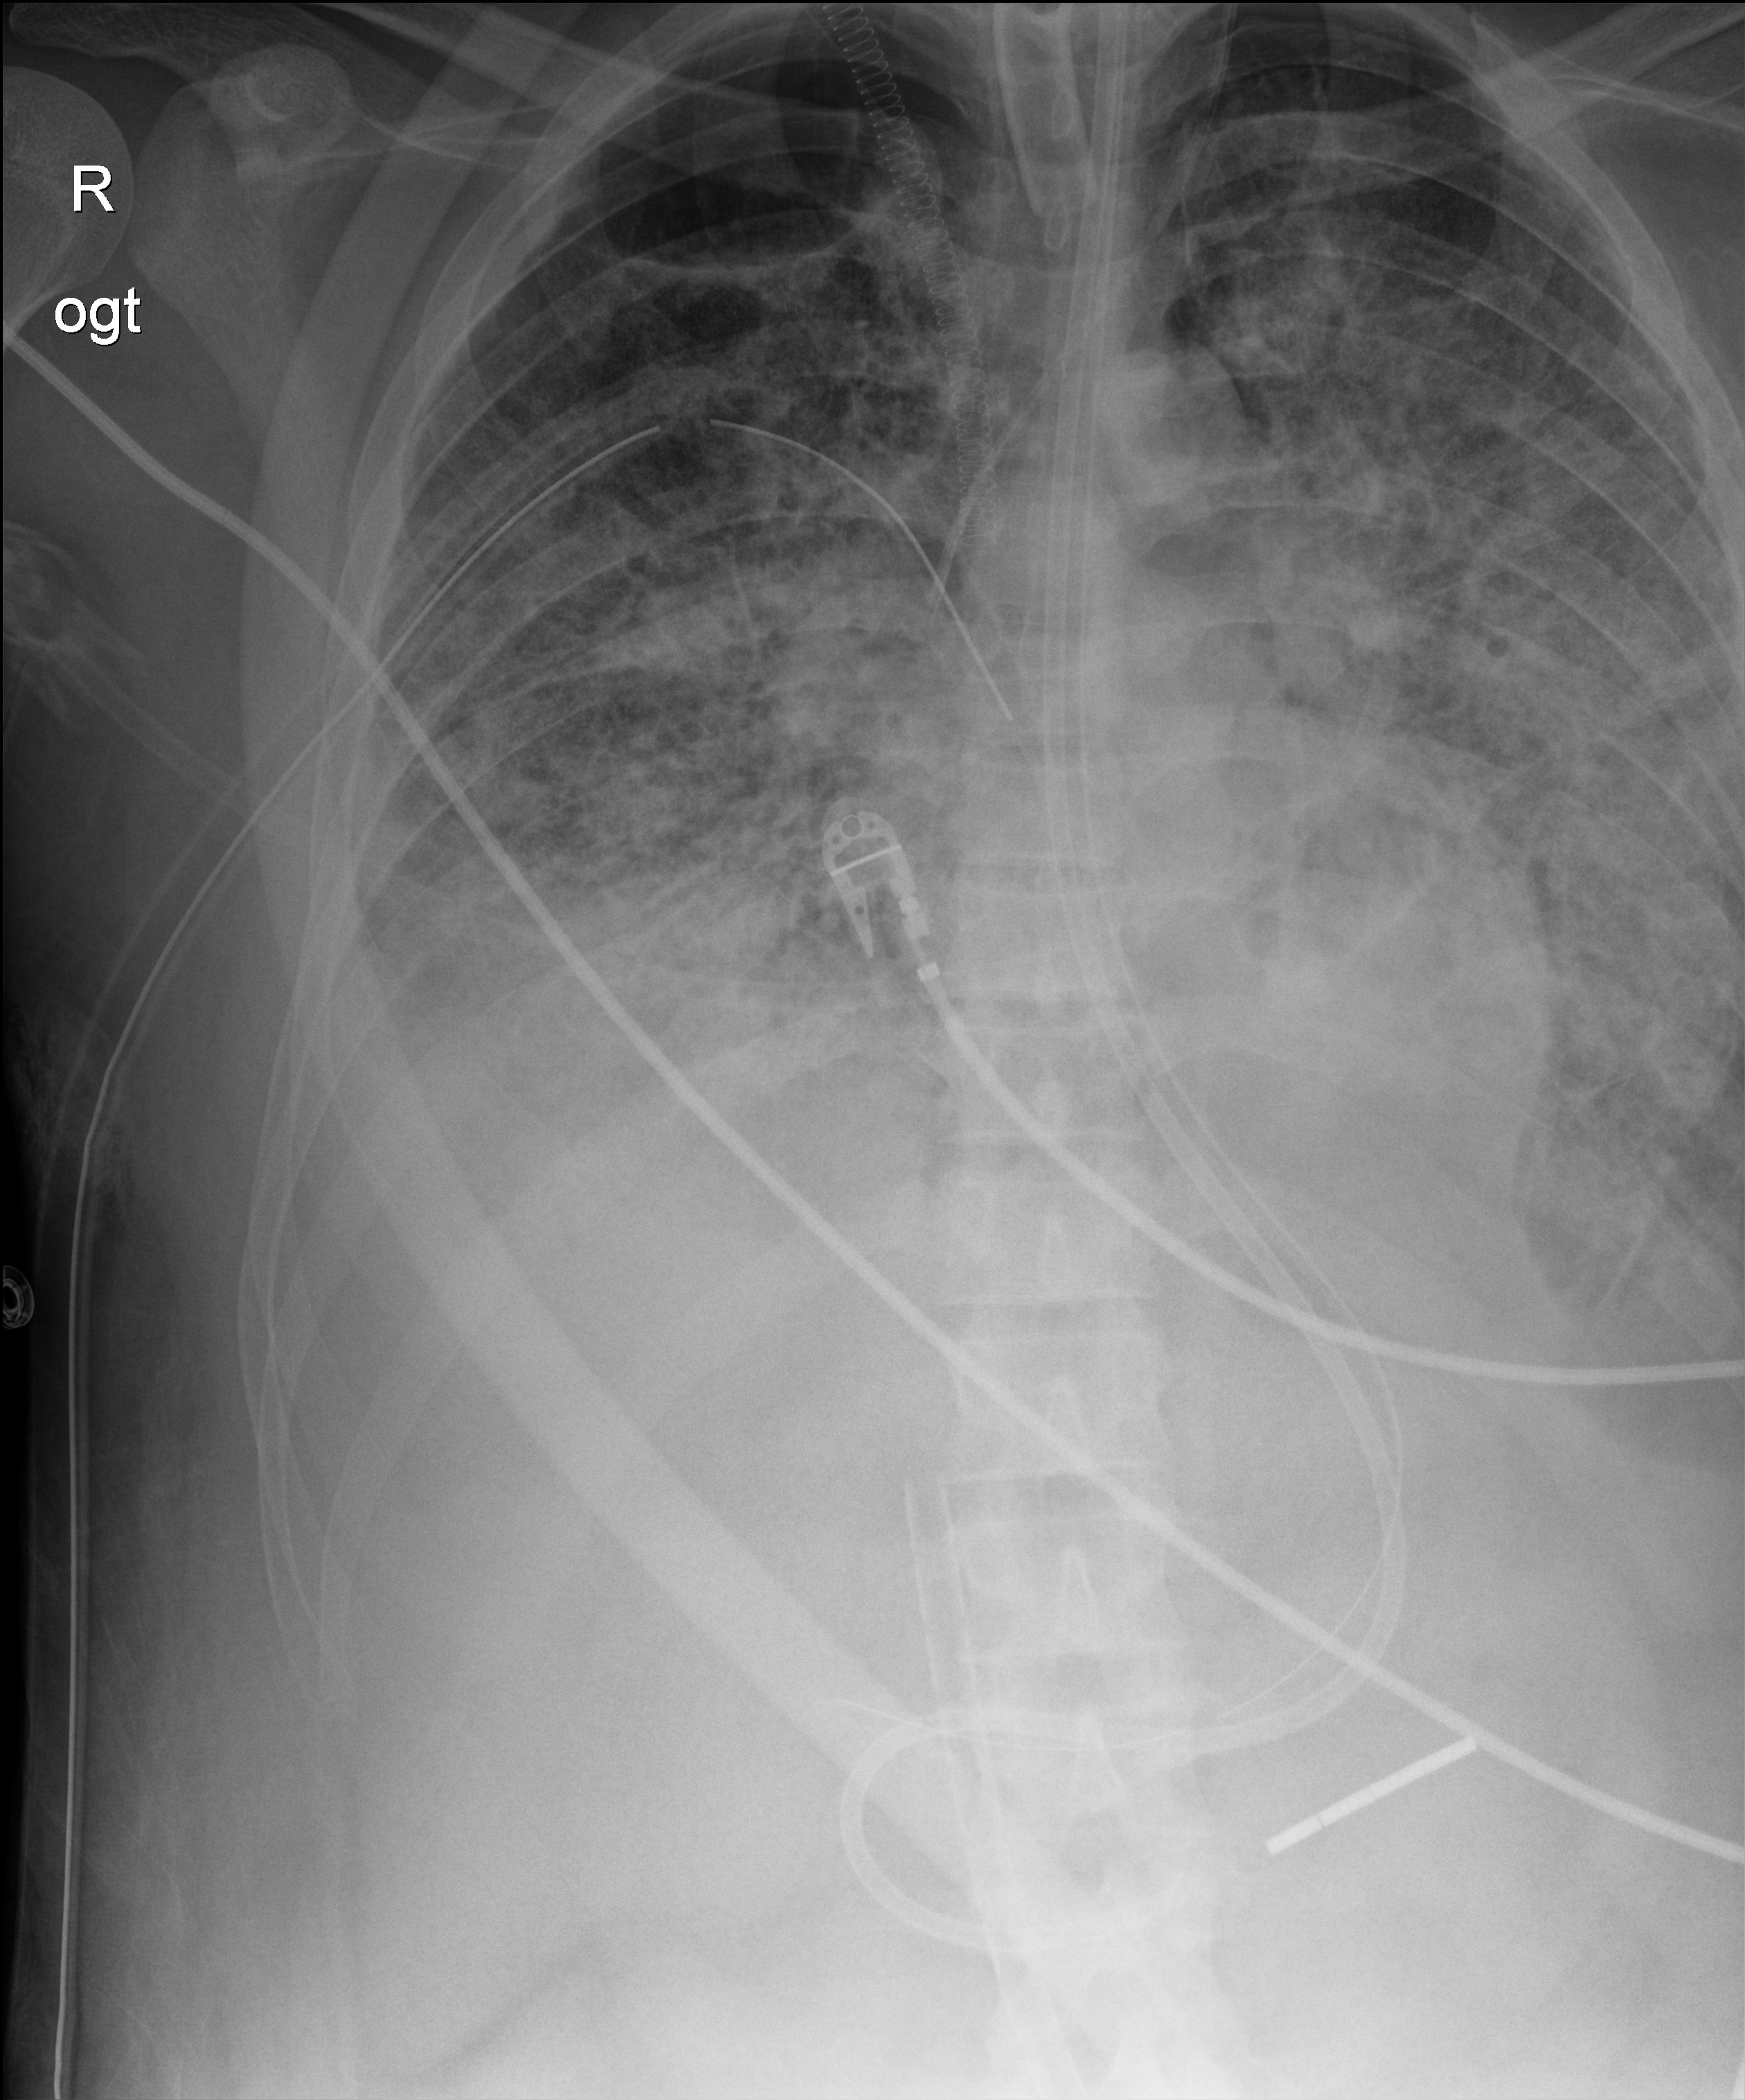
Chest X-ray, anteroposterior (AP) projection. Adult patient hospitalised with COVID-19, age 18–59 years.
From the hospital-stay record, not from the radiograph (when in the stay this image was taken is not recorded):
- length of hospital stay: 60 days
- diabetes (admission record): no